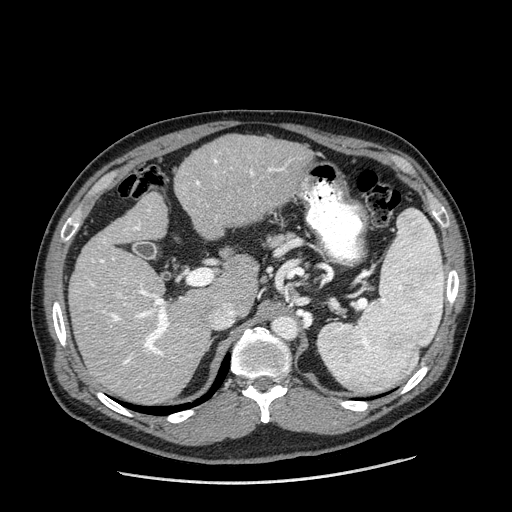
Contrast-enhanced abdominal CT (liver protocol), one axial slice. Slice 113 of 198 in the series (ordered by position). Reconstruction kernel STANDARD. One of 2 acquisitions stored at this slice position. Soft-tissue window (W 400 / L 40 HU). 512 × 512 image matrix, field of view 400 × 400 mm. Case-level facts recorded for this patient, not image findings: diagnosis: hepatocellular carcinoma (patient treated with transarterial chemoembolisation; whether this scan precedes or follows treatment is not stated here); TNM stage (as recorded): Stage-II; Child-Pugh class: A; tumour differentiation: moderately differentiated; tumour nodularity: multinodular.
Structures marked on this image (semi-automatic segmentation, software-assisted and operator-edited):
- liver parenchyma outside the tumour (the mass and vessels are separate outlines, so this box may not span the whole liver): bounding box <68,134,312,404> (left, top, right, bottom; pixels)
- liver vessels: <90,159,284,387>